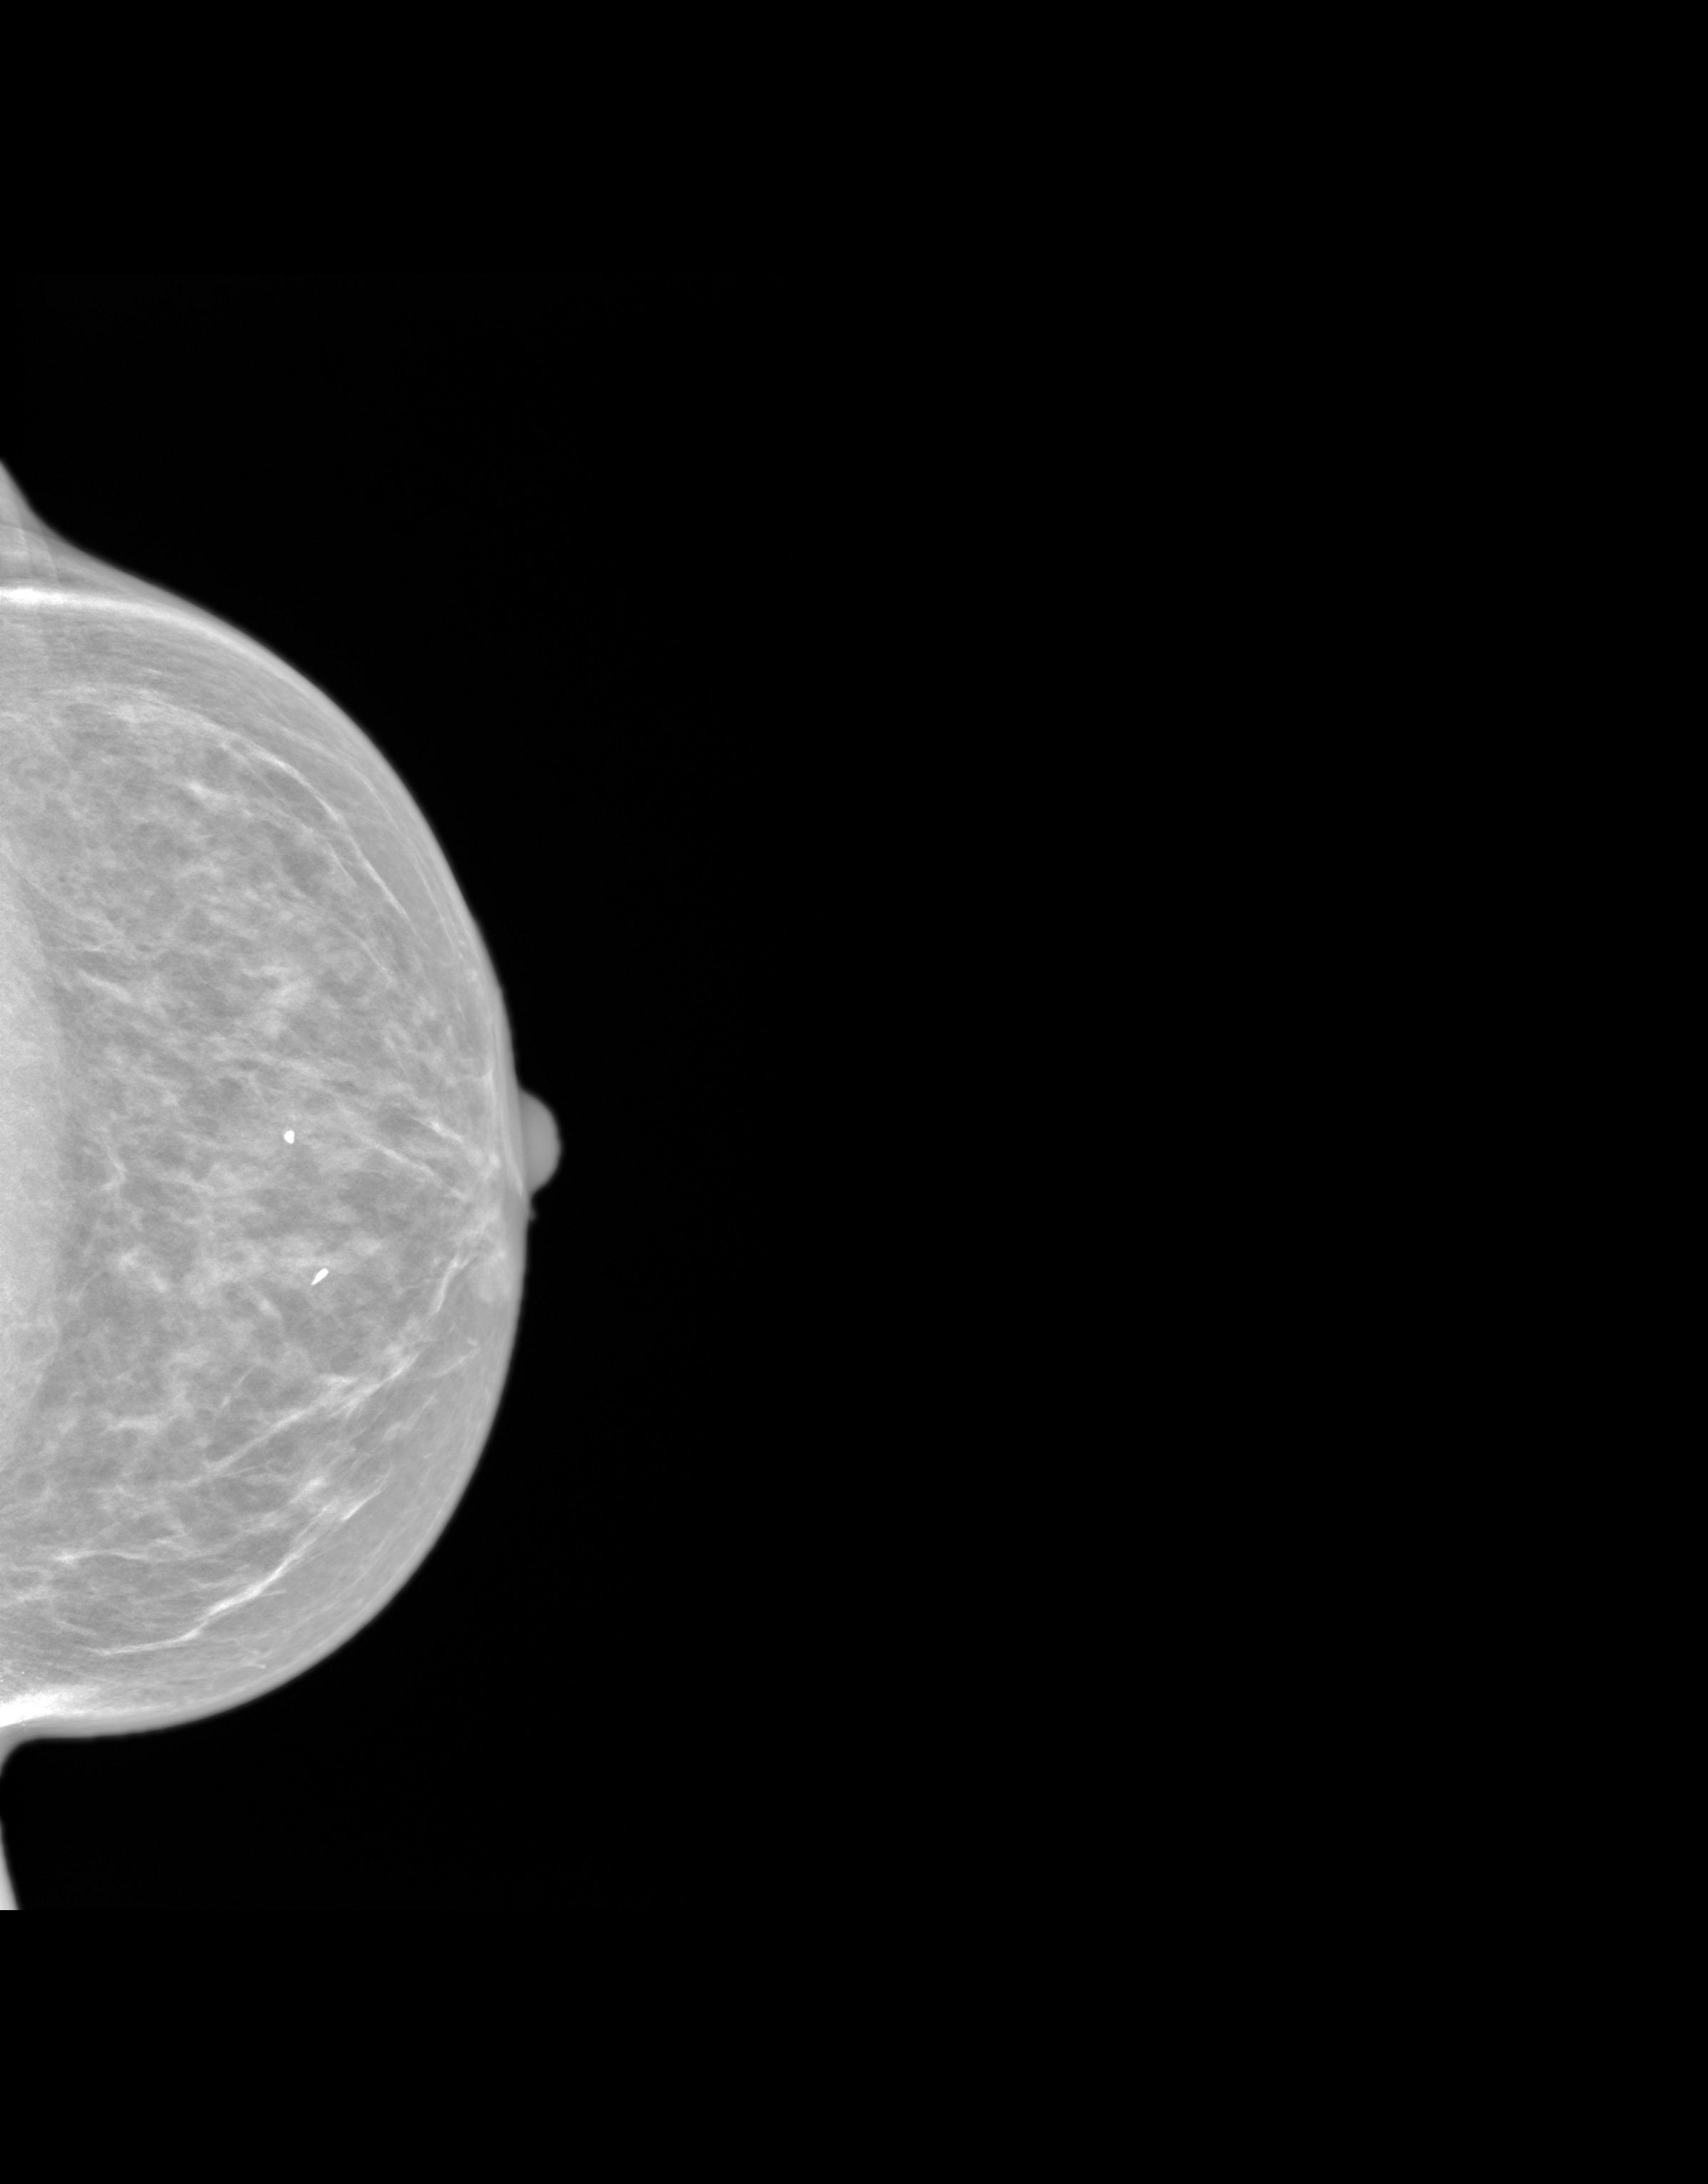
Synthetic 2-D view generated from a tomosynthesis acquisition (not an FFDM exposure); left breast; craniocaudal (CC) view; screening examination. Patient: female, 69 years.
Breast density at the screening exam (both breasts): heterogeneously dense (BI-RADS density category c). Final BI-RADS assessment for this screening round (tomosynthesis exam, both breasts): category 1. Recall: no recall after this screen.